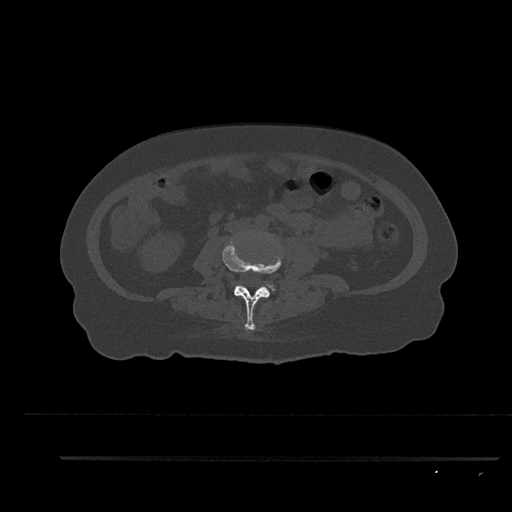
CT including the spine, one axial slice. Slice 67 of 797 in the series (ordered by position). Reconstruction kernel Br40s/3. Bone window (W 1800 / L 400 HU). 512 × 512 image matrix, field of view 408 × 408 mm. Patient: female, 44 years. Case-level facts recorded for this patient, not image findings: primary cancer: renal; vertebrae with lytic lesions (as recorded): L1.
Outlined on this slice (semi-automatic segmentation, software-assisted and operator-edited):
- L3 vertebra: box from (x=222, y=238) to (x=282, y=330) px
- L4 vertebra: (x=262, y=284)–(x=276, y=292)